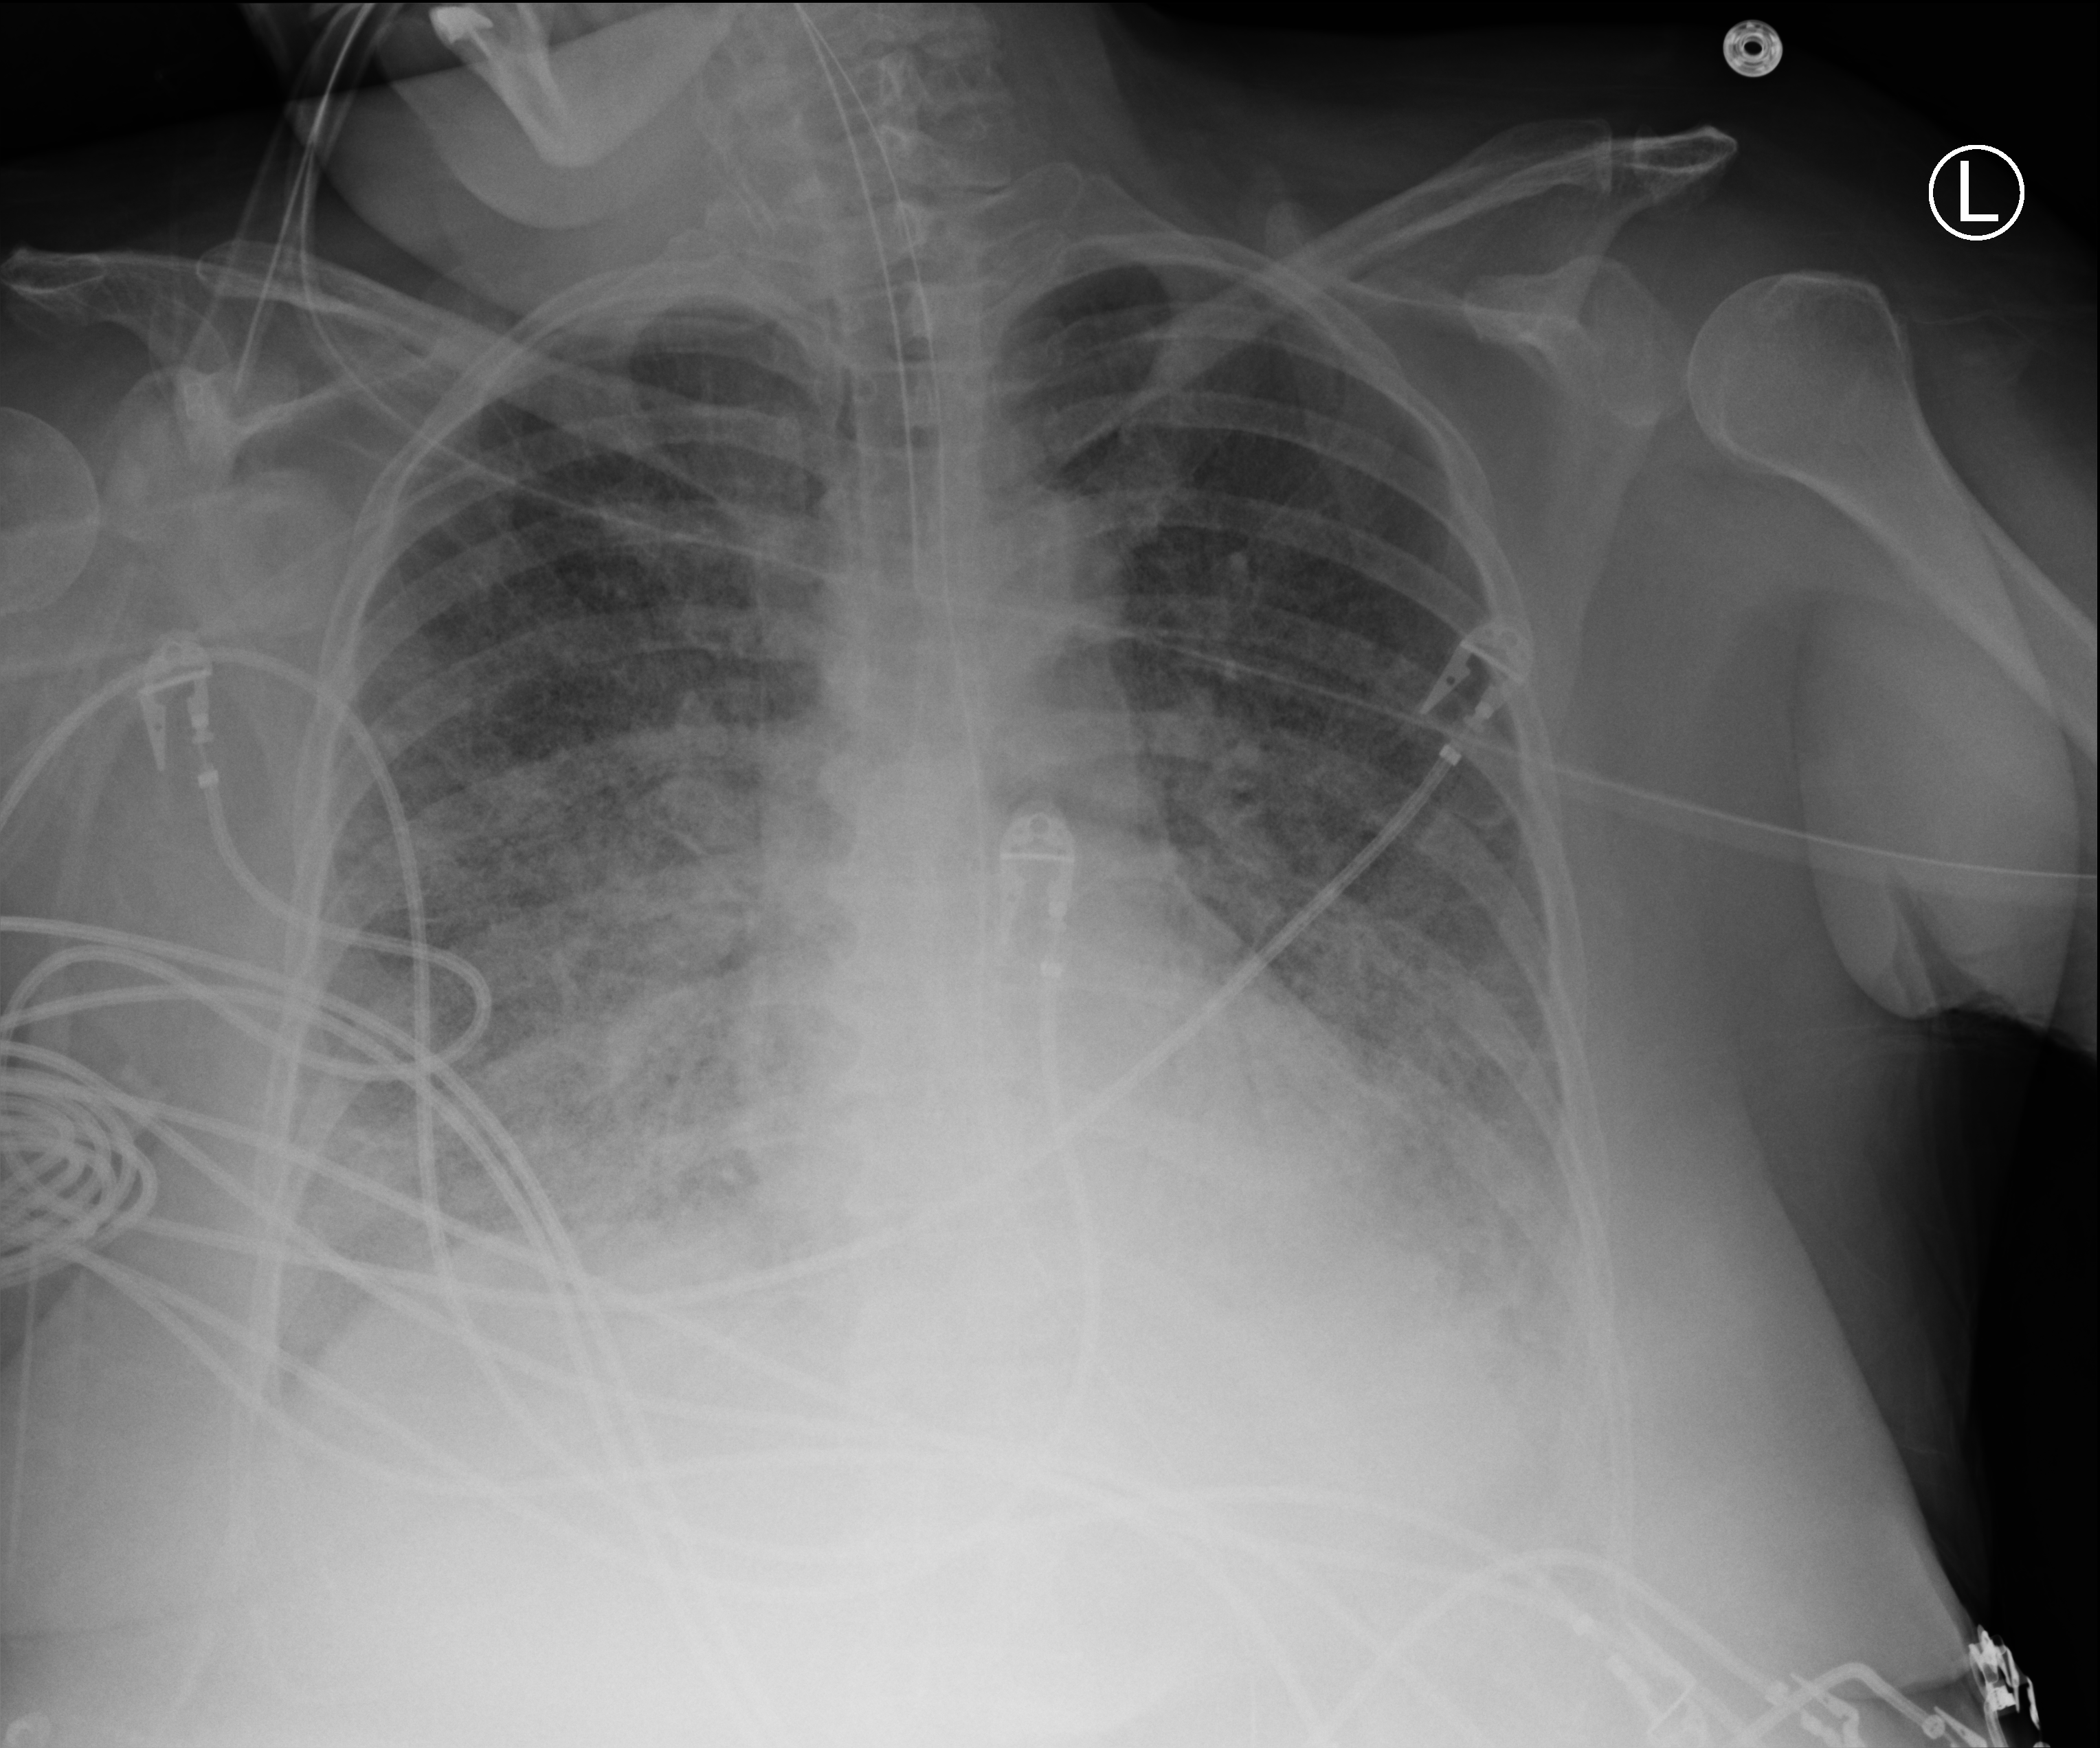
Portable chest radiograph; anteroposterior (AP) projection. Female patient hospitalised with COVID-19, age 60–74 years.
From the hospital-stay record, not from the radiograph (when in the stay this image was taken is not recorded): smoking status (admission record): former; hypertension (admission record): no.